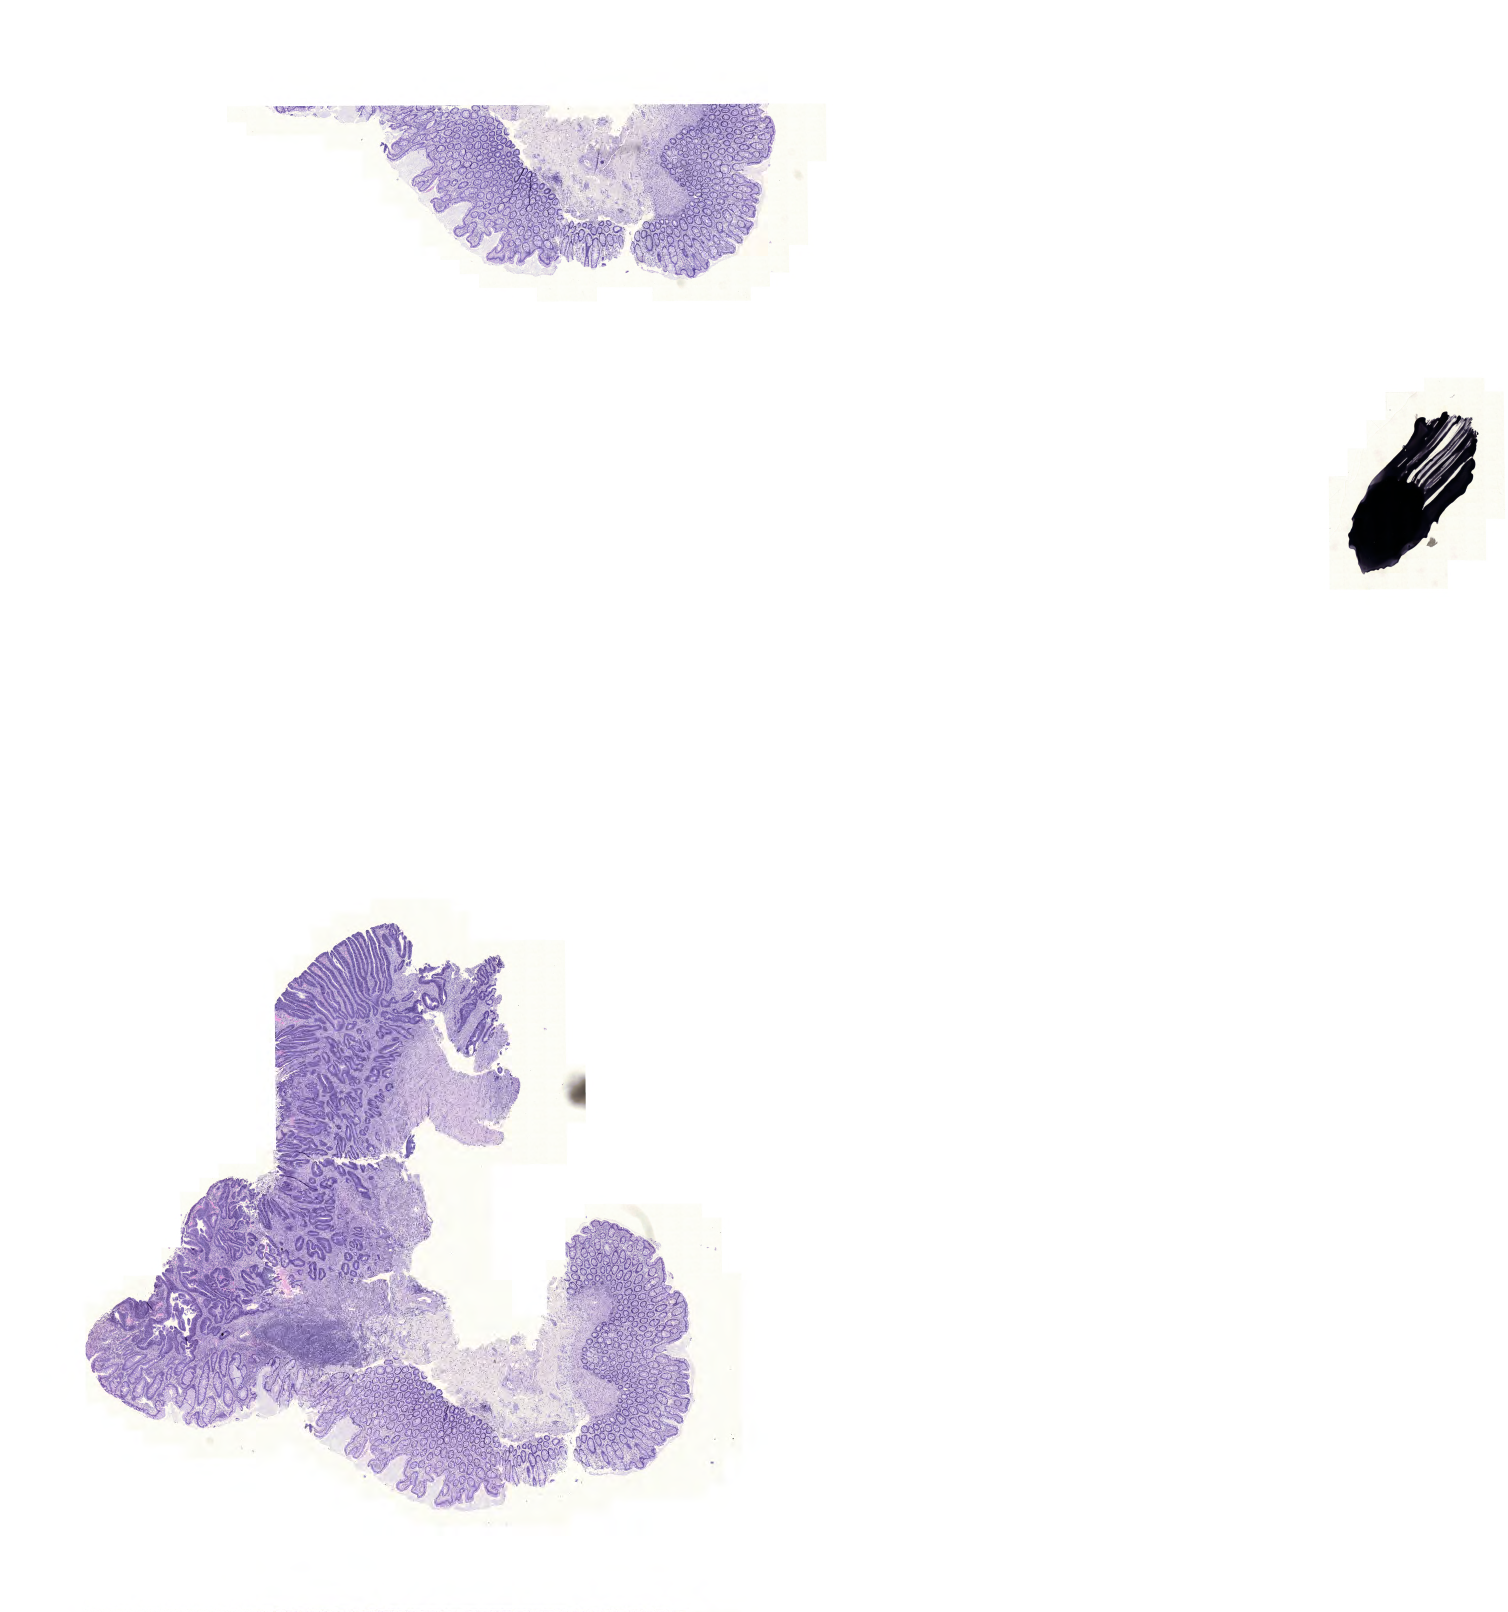
H&E-stained whole-slide image — shown as a low-resolution overview of the whole scanned area (about 22.4 x 24.0 mm, slide scanned at 20x). FFPE section. Colon, primary tumour sample. Patient: female, age at initial diagnosis 61 years.
Diagnosis: Adenocarcinoma, NOS (sigmoid colon).